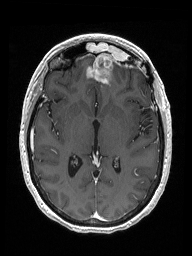
Brain MRI from a brain-tumour surgery series, one axial slice; slice 86 of 192 in the series (ordered by position); T1-weighted post-contrast; 1 mm slice thickness; 192 × 256 image matrix, field of view 187 × 250 mm. Case-level facts recorded for this patient, not image findings: histopathology: Metastastic Carcinoma from Breast primary; tumour location: Right Frontal.
Outlined on this slice (manually delineated by an expert):
- previous resection cavity: box from (x=110, y=74) to (x=111, y=79) px